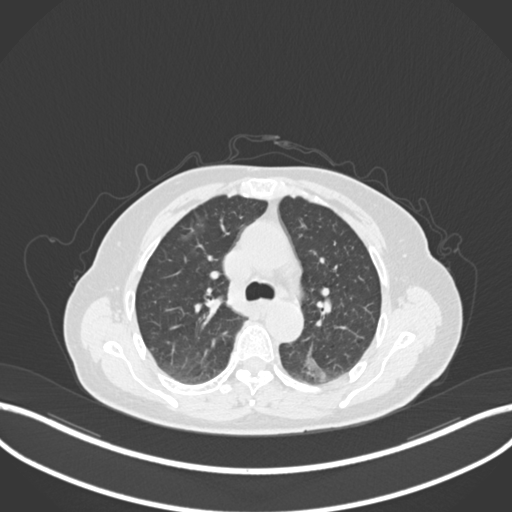
Chest CT, one axial slice. Position 546 of 727 along the scan axis. Reconstruction kernel B30f. Lung window (W 1500 / L -600 HU). 1 mm slice thickness. 512 × 512 image matrix, field of view 400 × 400 mm. Female patient, age 70 years. From the clinical record (not read from this slice): clinical TNM (as recorded): T1c N0 M0.
Annotated regions visible in this slice (bounding box drawn by a radiologist):
- lung tumour (recorded histology: adenocarcinoma): bounding box <306,353,330,385> (left, top, right, bottom; pixels)